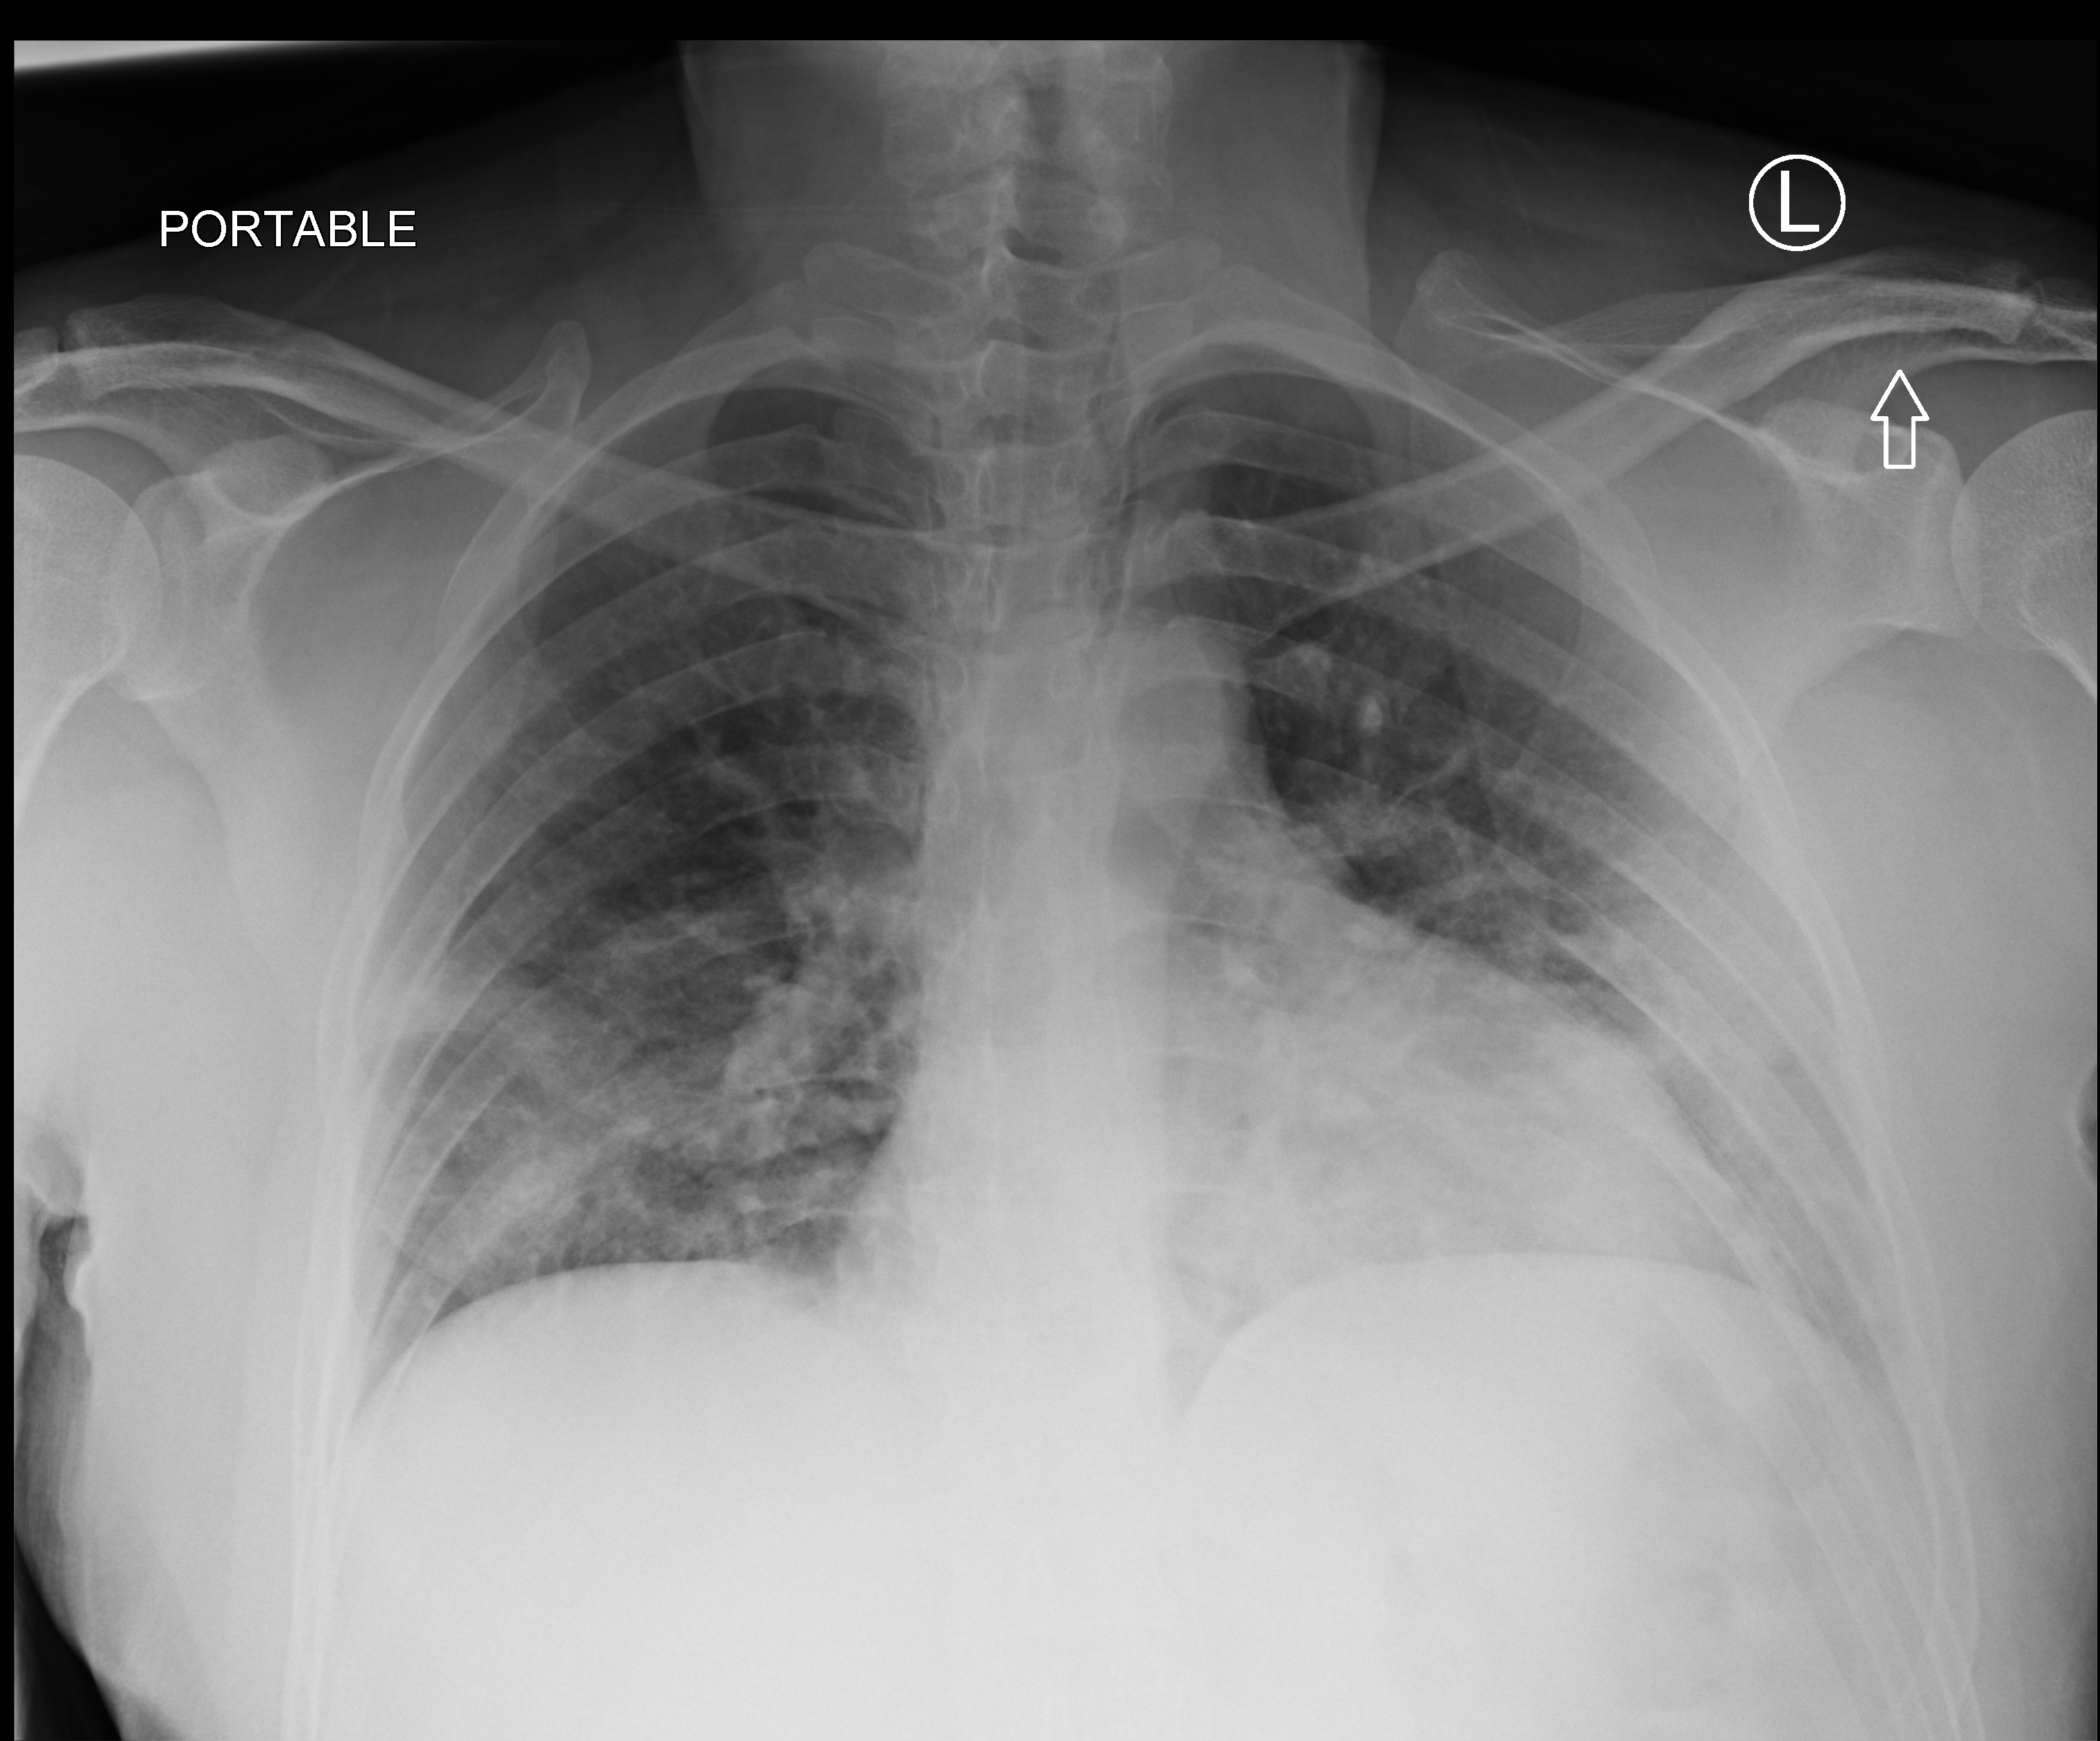
Portable chest radiograph. Patient hospitalised with COVID-19; male, aged 18–59 years.
Hospital-stay facts (about this admission, not read from this image; timing relative to this image not recorded): COPD (admission record): no.